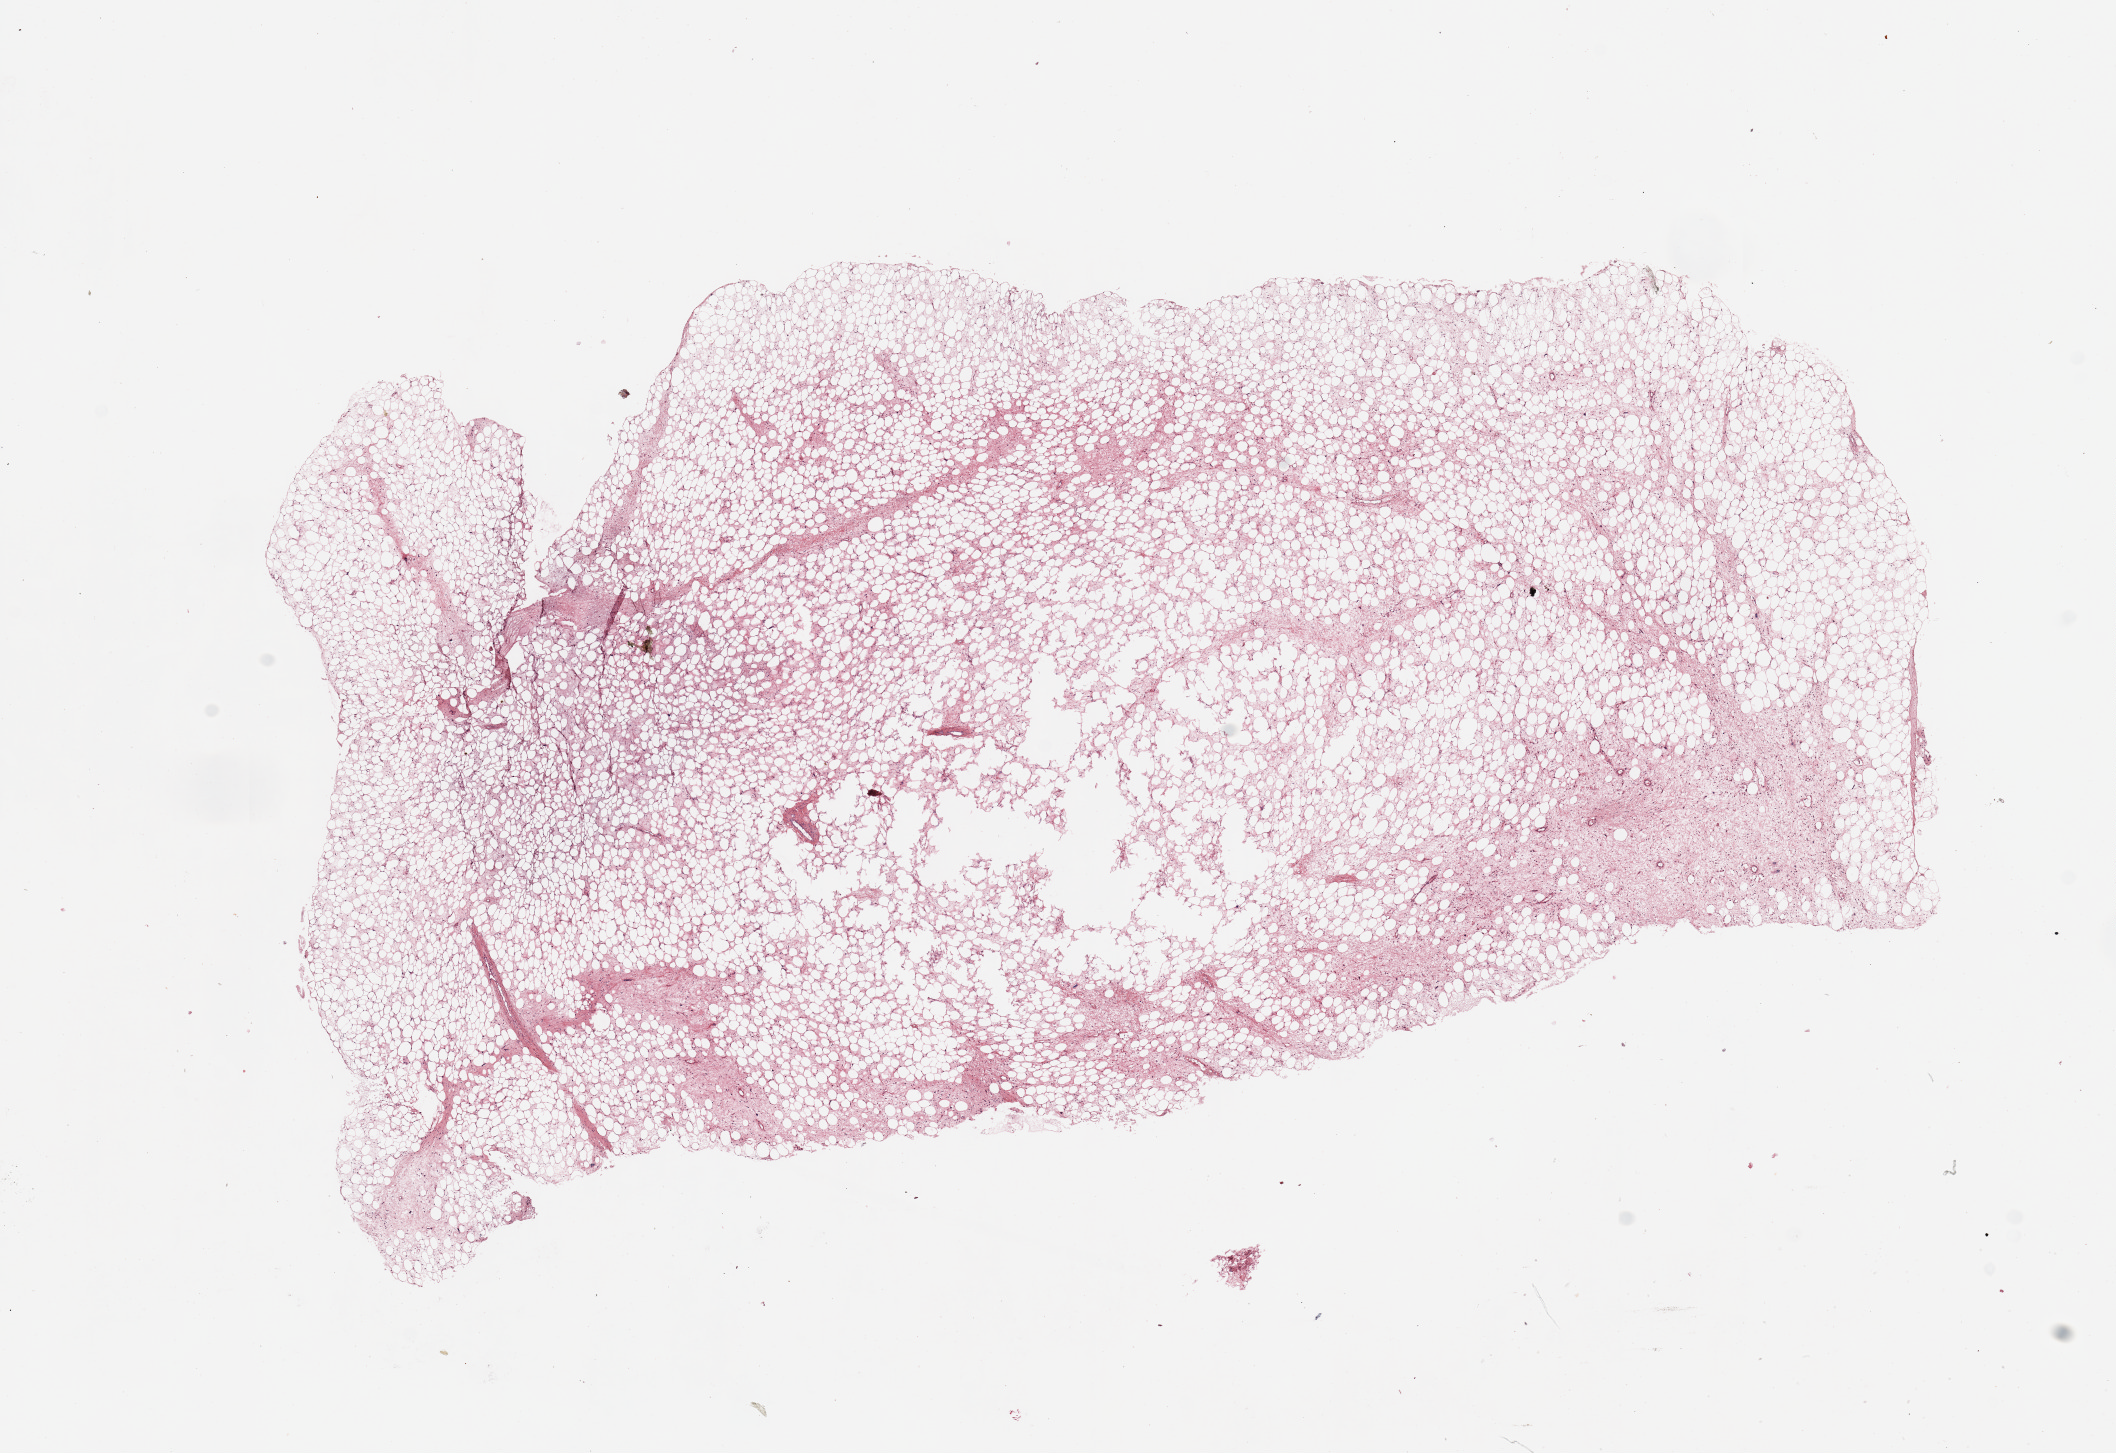
Digitized H&E tissue section (whole slide), low-resolution overview of the scanned area, about 16.7 x 11.5 mm. Tumour tissue sample. Patient: female, age 65 years.
- primary tumour site (as recorded): retroperitoneum
- patient diagnosis (cohort enrolment): sarcoma (site not recorded at cohort level)